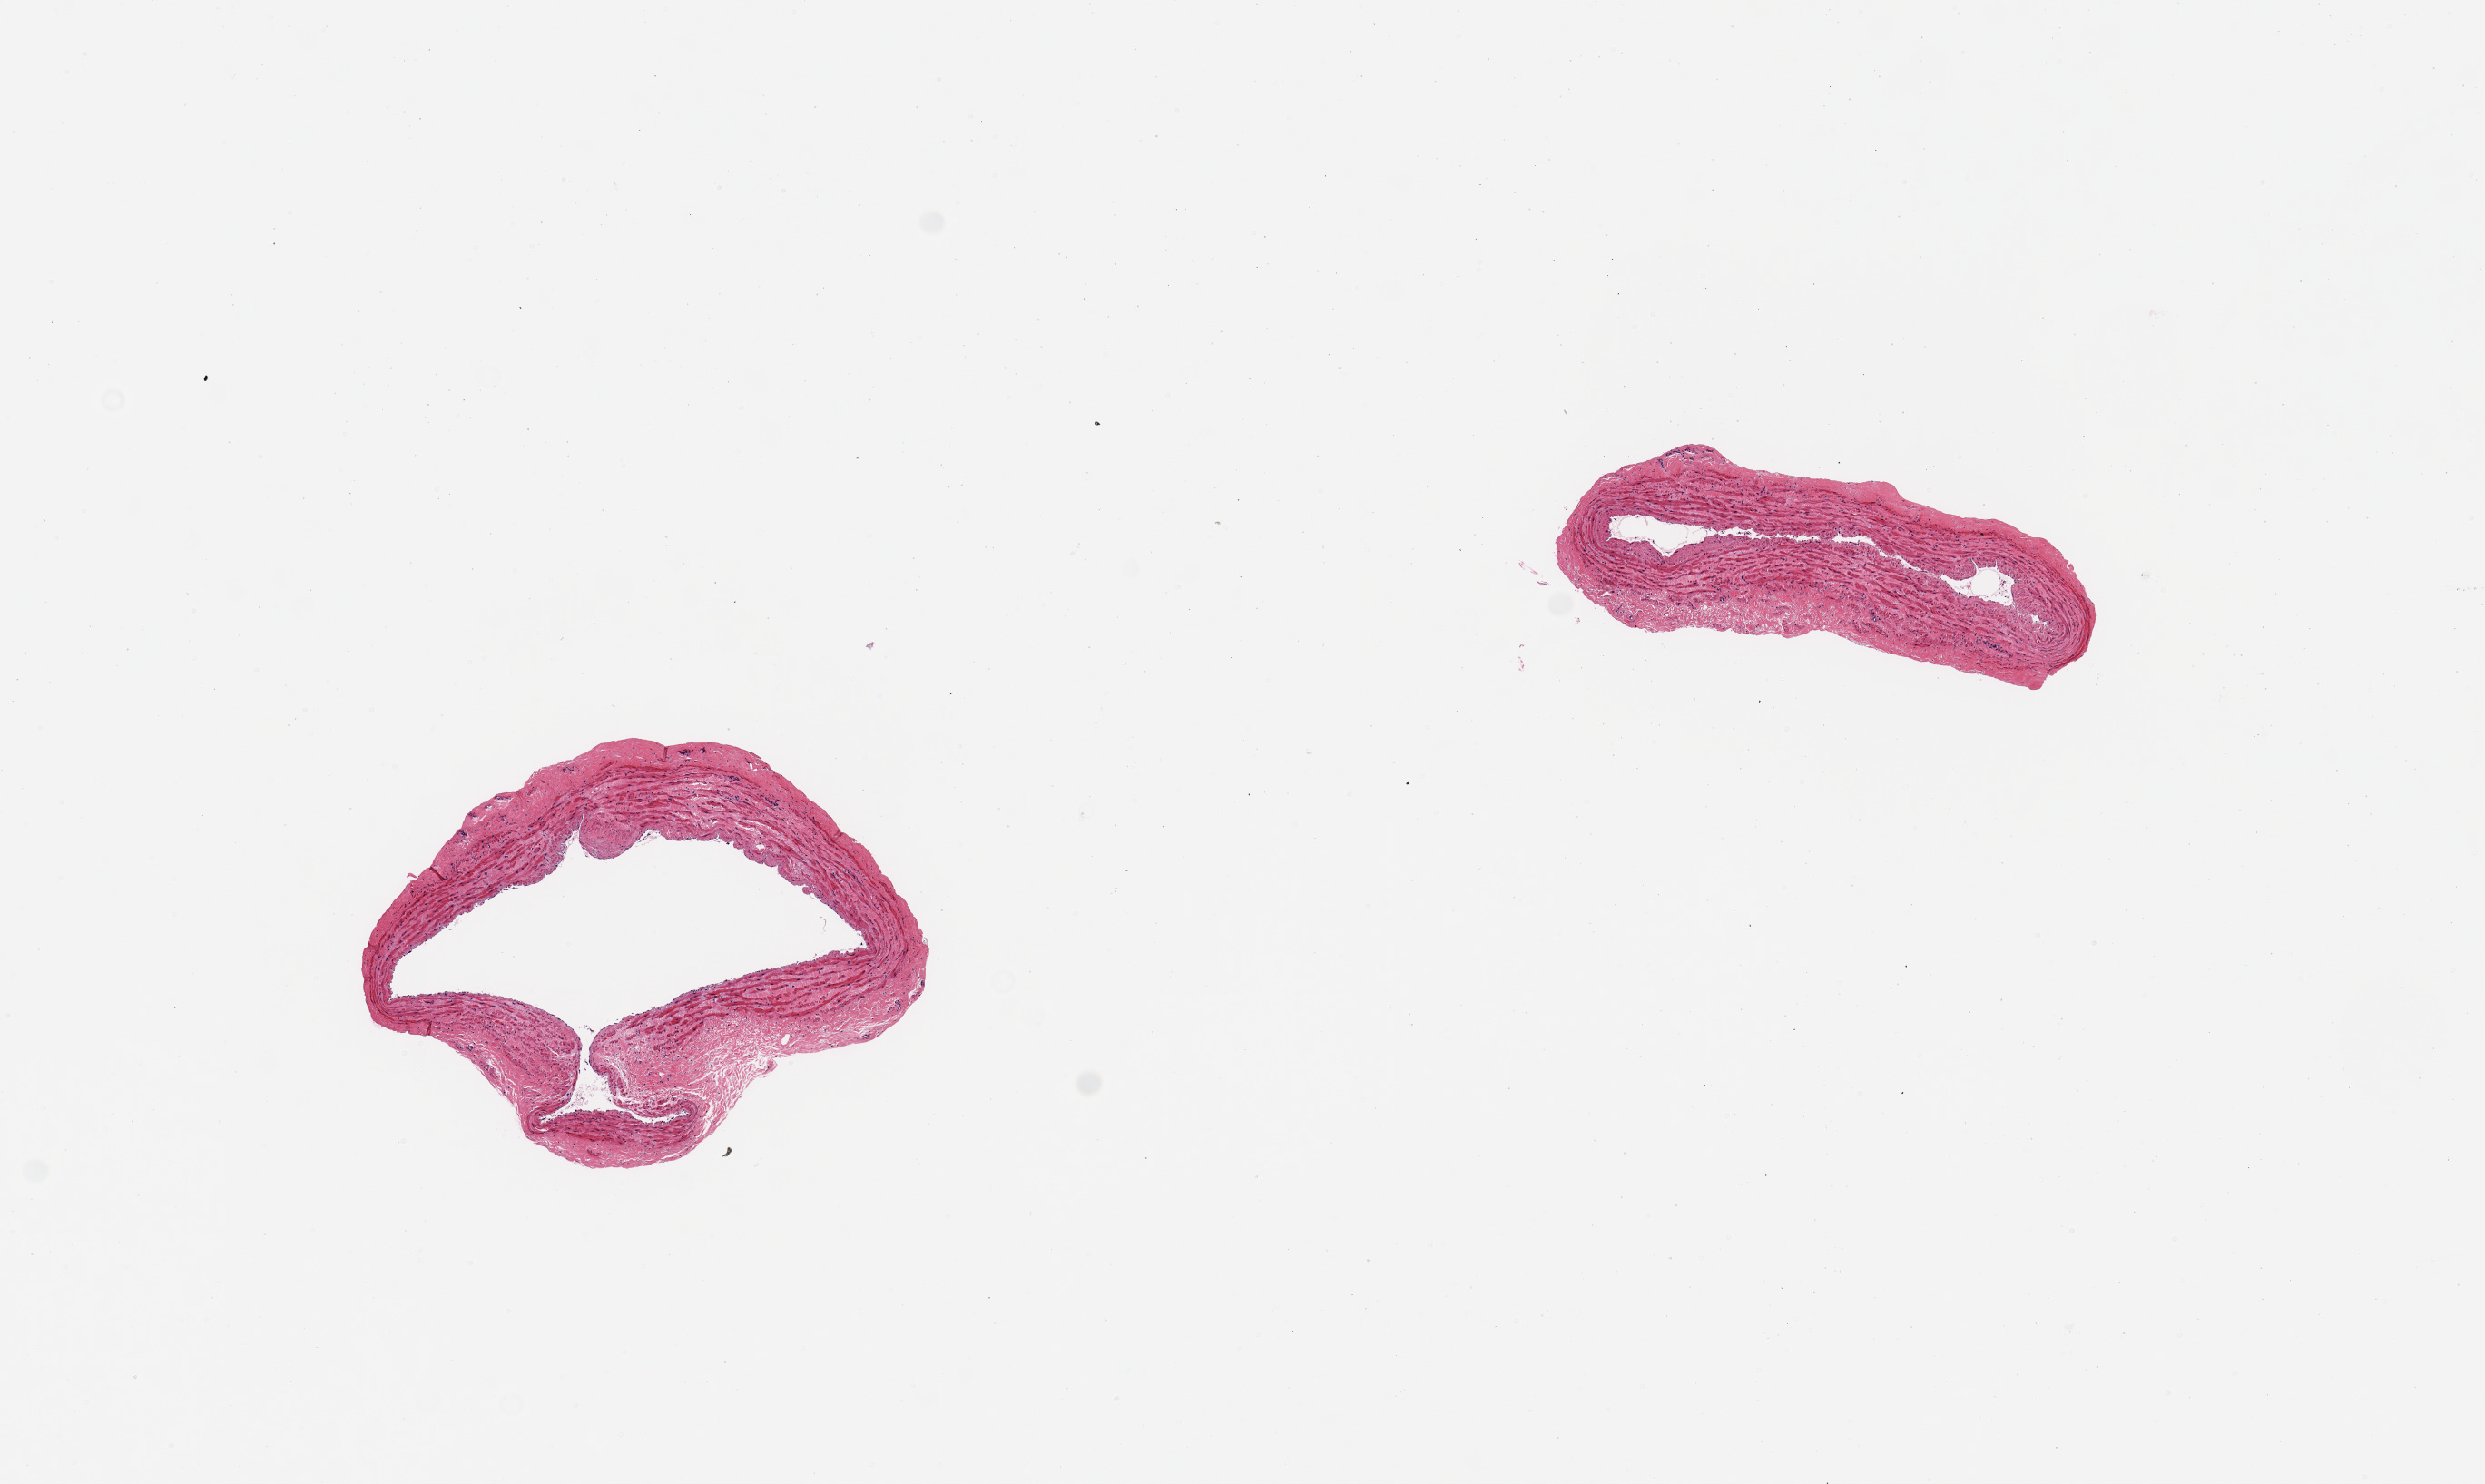
H&E whole-slide image, brightfield, shown as a low-resolution overview of the whole scanned area (about 10.8 x 6.5 mm). PAXgene-fixed, paraffin-embedded tissue. Section of tibial artery (target tissue). Donor tissue sample. Donor sex: male.
Pathologist's review note for this sample: 2 pieces; well trimmed; no plaques.